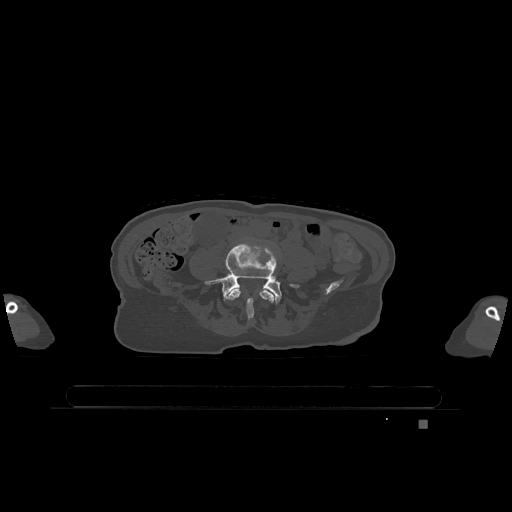
CT including the spine, one axial slice; bone window (W 1800 / L 400 HU); 512 × 512 image matrix, field of view 500 × 500 mm. Female patient, age 74 years. From the clinical record (not read from this slice): primary cancer: lung; vertebrae with lytic lesions (as recorded): T1, T4, T5, T6, L4, L5.
Structures marked on this image (semi-automatic segmentation, software-assisted and operator-edited):
- L4 vertebra: bounding box <227,289,274,320> (left, top, right, bottom; pixels)
- L5 vertebra: <205,244,299,304>